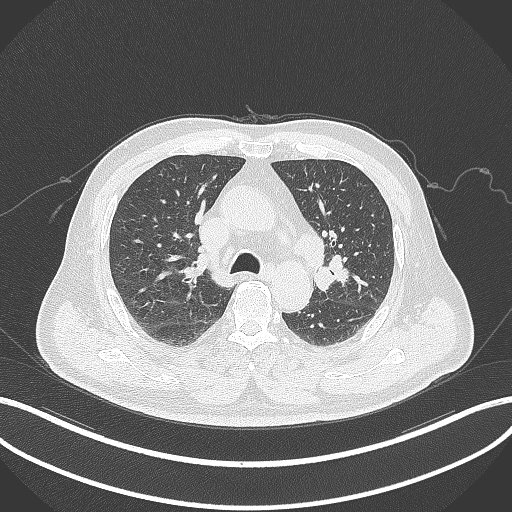
Chest CT, one axial slice; slice 199 of 286 in the series (ordered by position); reconstruction kernel B70f; 120 kVp; lung window (W 1500 / L -600 HU); 1 mm slice thickness; 512 × 512 image matrix. Patient: male, 67 years. Case-level facts recorded for this patient, not image findings: clinical TNM (as recorded): T2a N1 M0.
Outlined on this slice (rectangle marked by the reading radiologist):
- lung tumour (recorded histology: adenocarcinoma): bounding box [x1, y1, x2, y2] px = [313, 254, 353, 292]